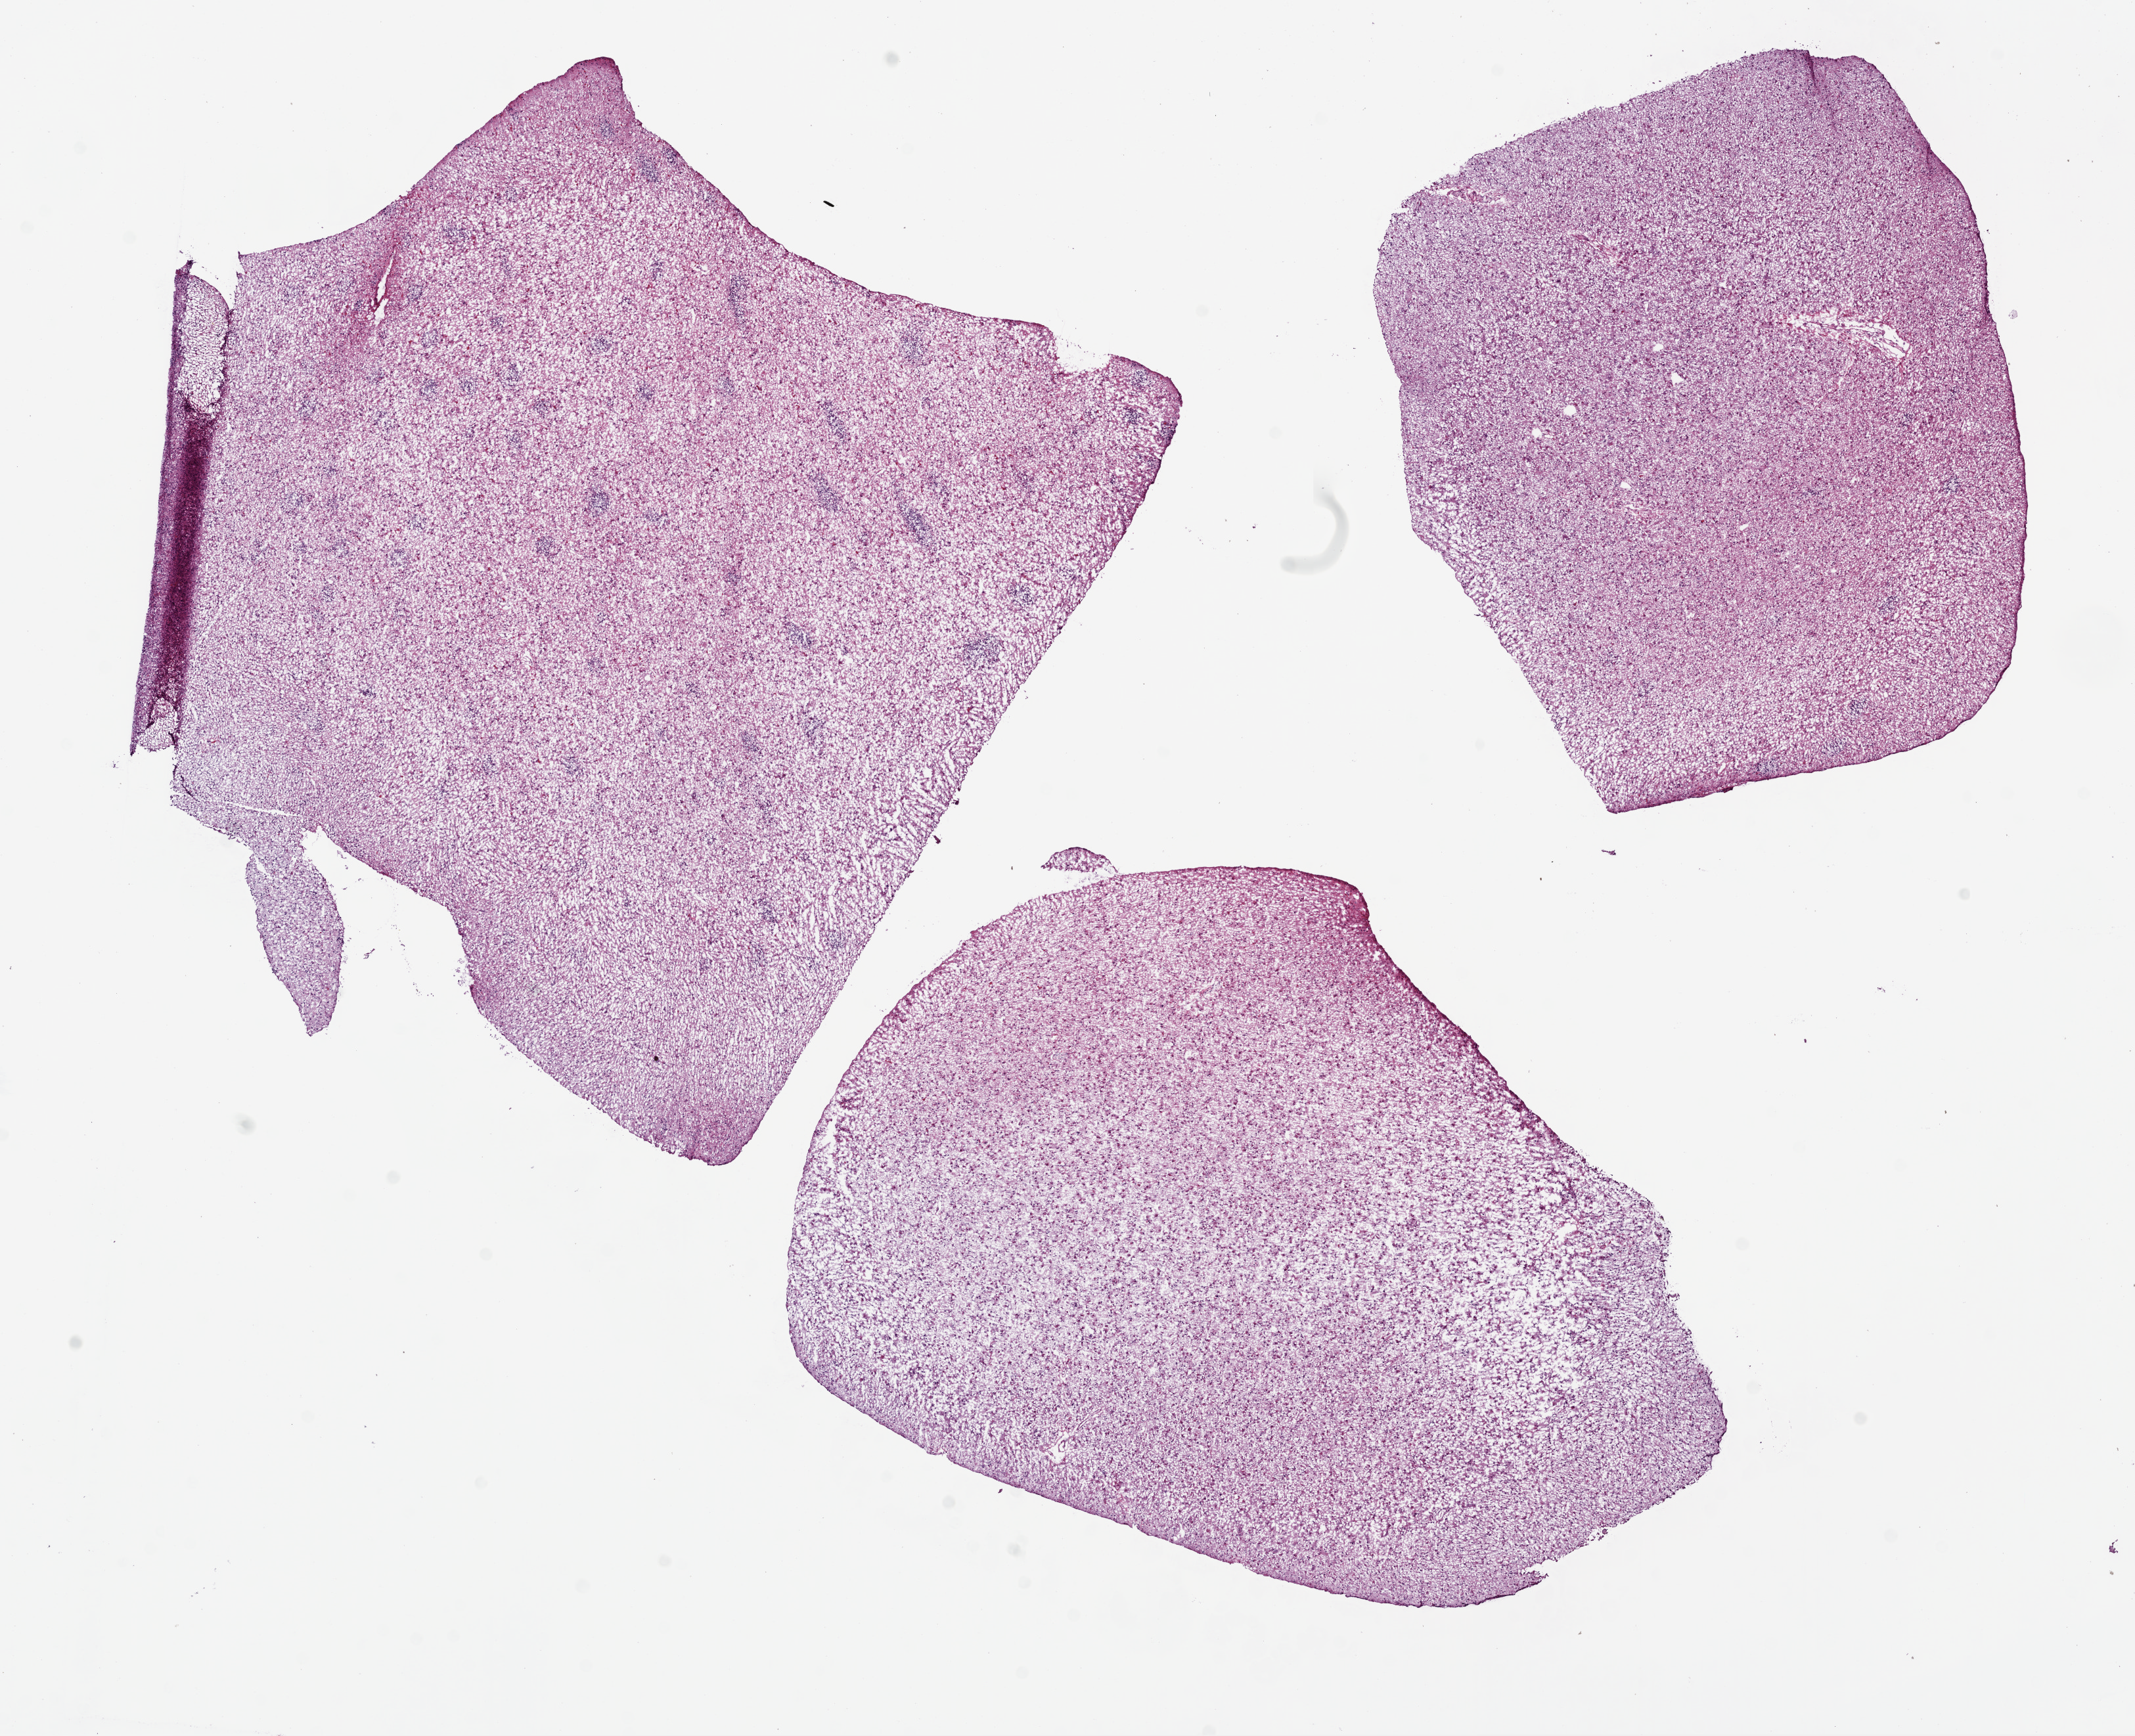
Whole-slide histology image, H&E-stained, whole scanned area (about 13.0 x 10.6 mm, from a 20x scan) shown as a low-resolution overview, frozen section, primary tumour sample from the brain. Male patient; age at initial diagnosis 41 years. Histologic grade: G3 (poorly differentiated). Composition of this section per pathologist review: tumour cells 100%, tumour nuclei 65%, normal cells 0%, stromal cells 0%, necrosis 0%.
- laterality: left
- diagnosis: Astrocytoma, anaplastic